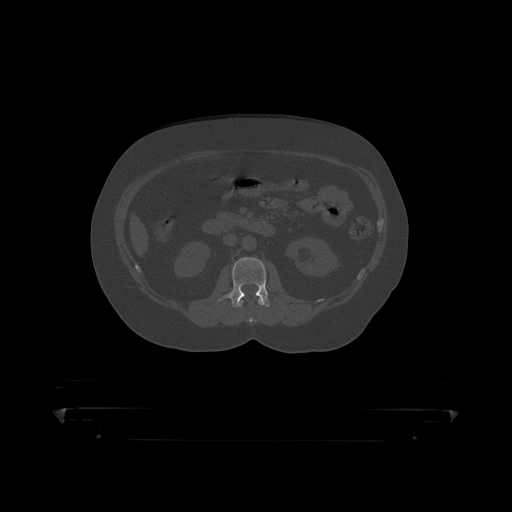
CT including the spine, one axial slice; slice 124 of 390 in the series (ordered by position); 120 kVp; bone window (W 1800 / L 400 HU); 1.25 mm slice thickness; 512 × 512 image matrix, field of view 650 × 650 mm. Patient: male, 60 years. Case-level facts recorded for this patient, not image findings: primary cancer: prostate.
Outlined on this slice (semi-automatic segmentation, software-assisted and operator-edited):
- L1 vertebra: bounding box (x1, y1, x2, y2) in pixels: (239, 299, 264, 319)
- L2 vertebra: (219, 258, 270, 309)